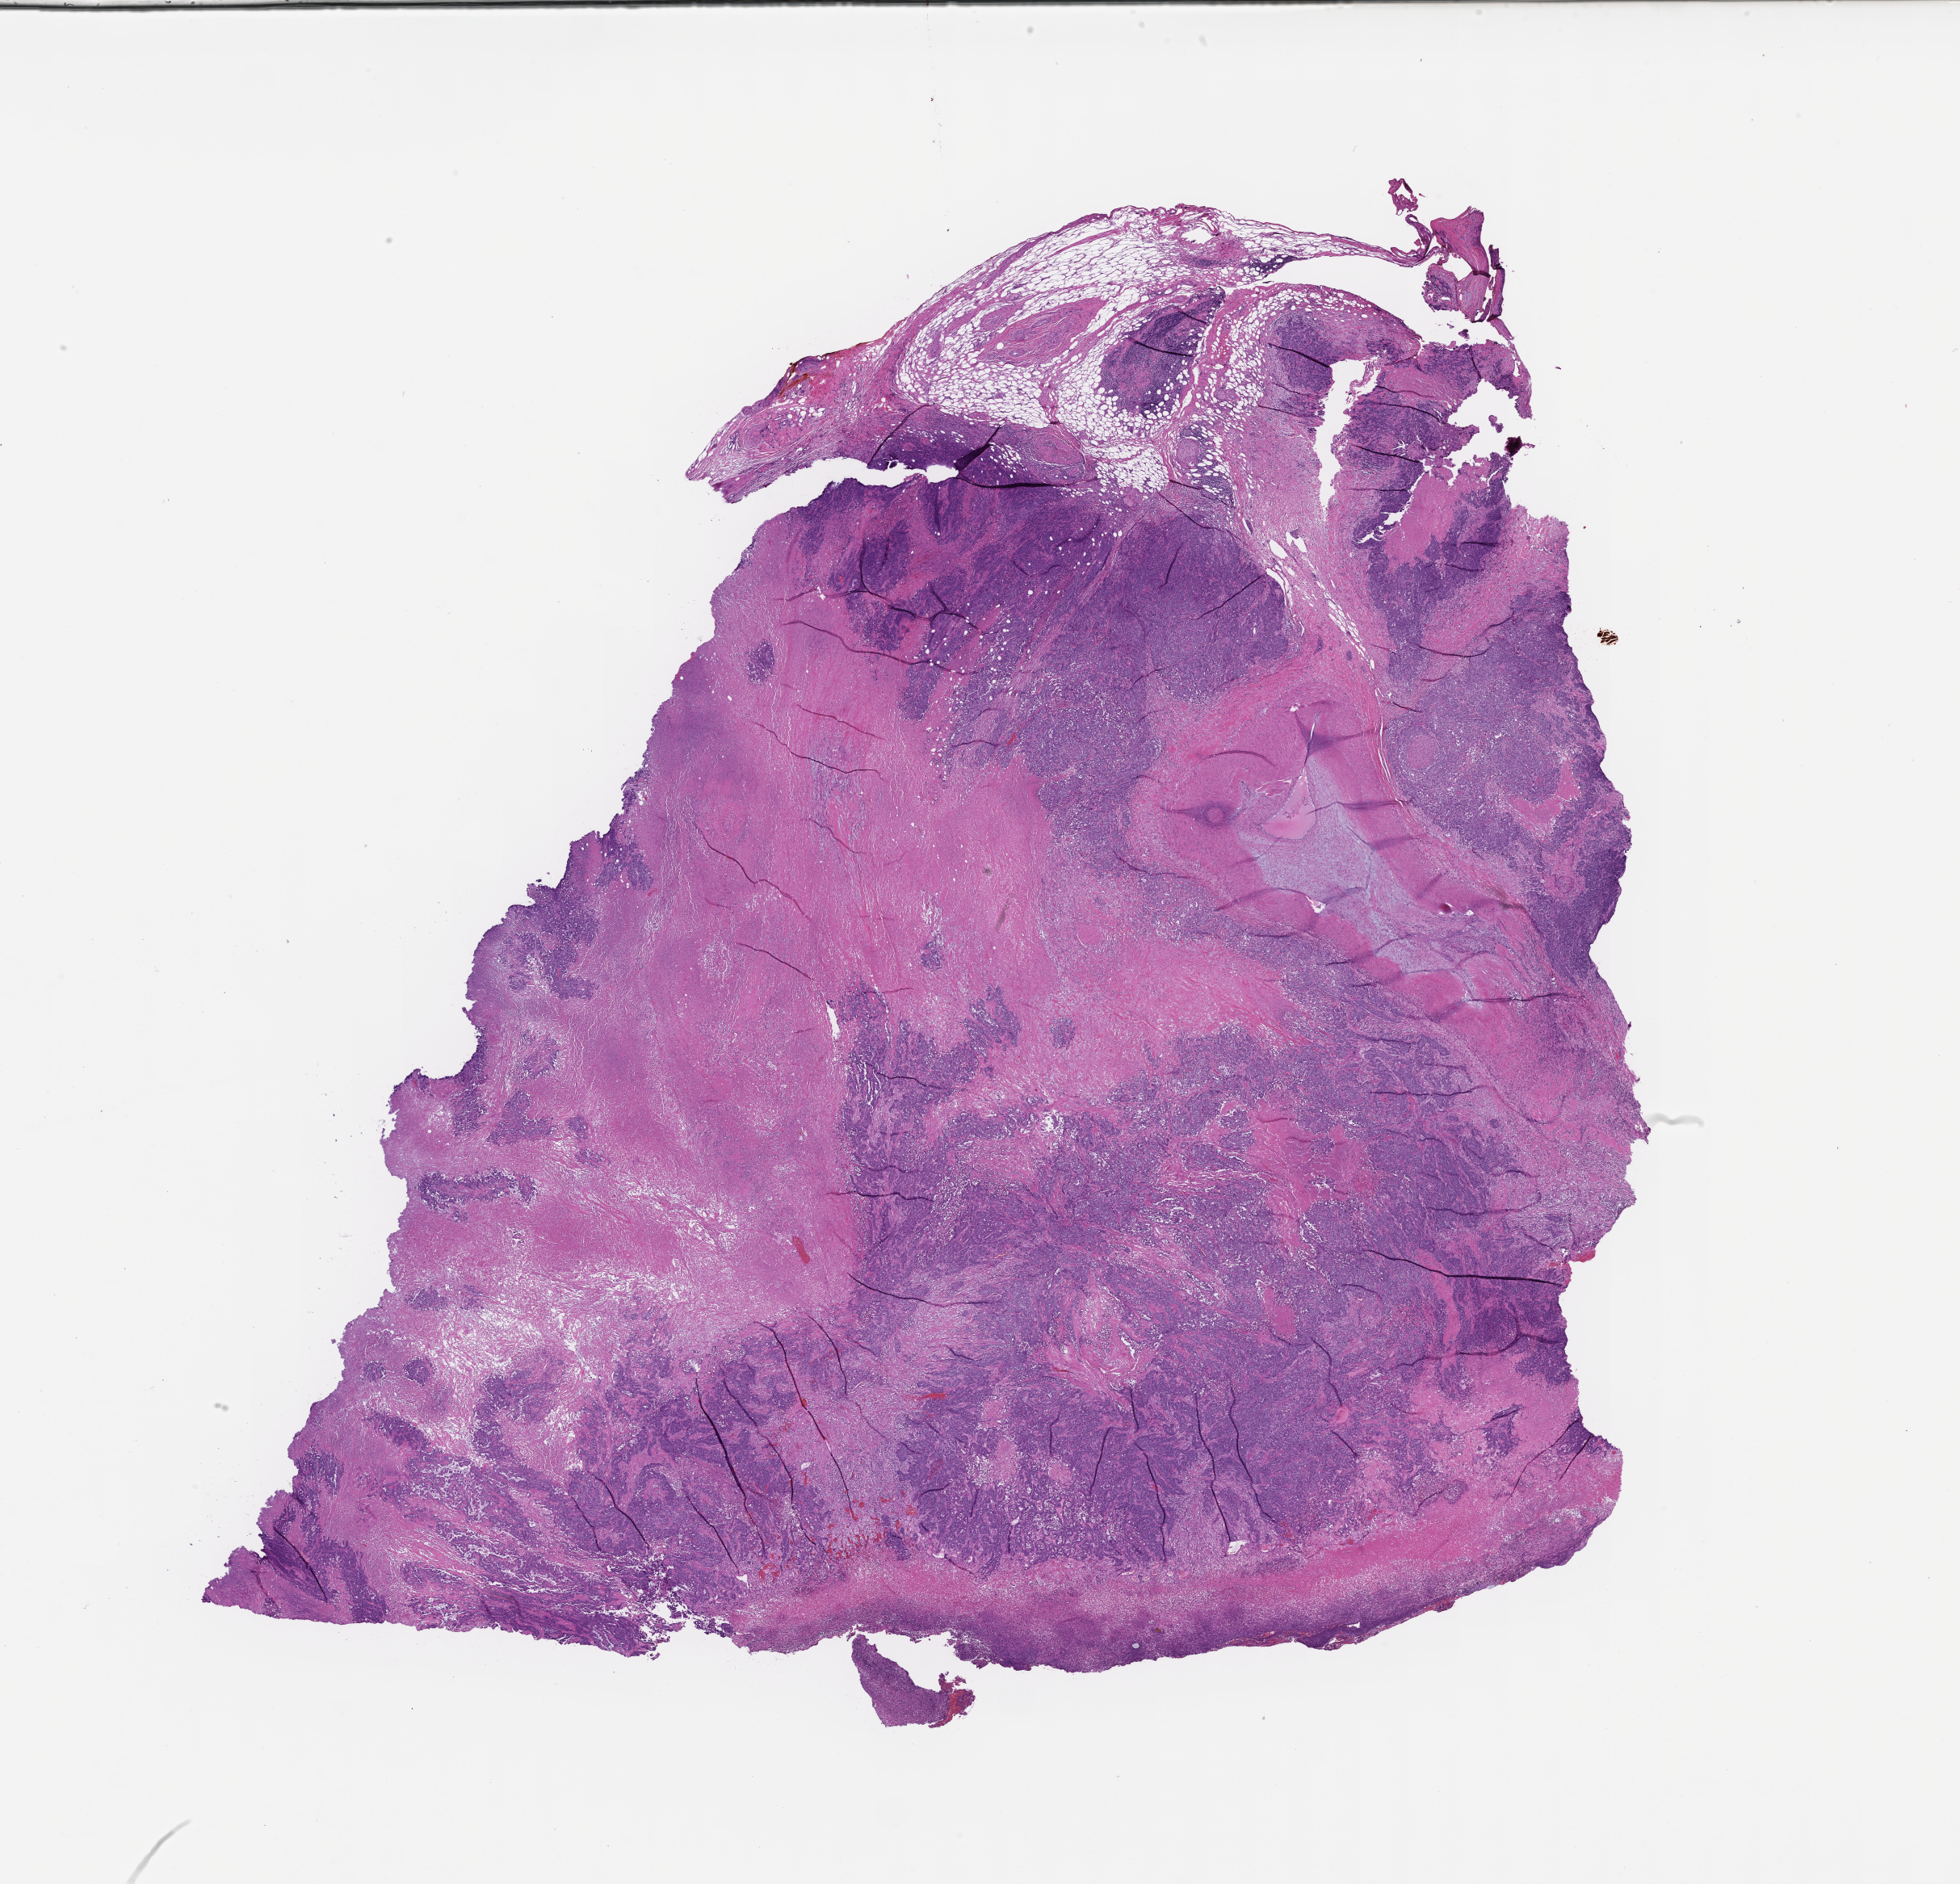
Whole-slide image, haematoxylin and eosin stain, low-resolution overview of the scanned area, about 19.6 x 18.8 mm. Formalin-fixed, paraffin-embedded (FFPE) tissue. Tissue site: colon. Archival tissue. Male patient.
This section: primary tumor. Diagnosis: Colorectal Carcinoma.